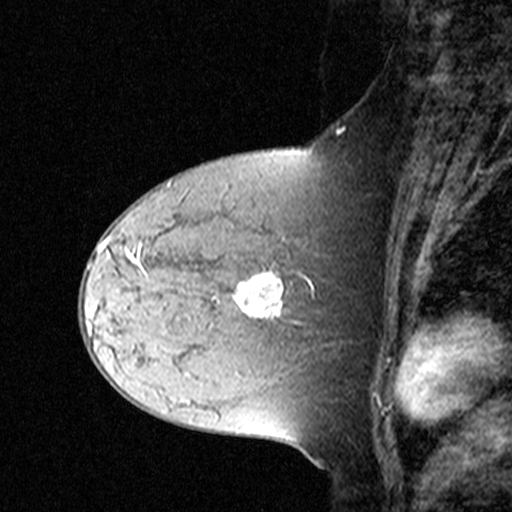
Breast MRI (dynamic contrast-enhanced), one sagittal slice; slice 17 of 44 in the series (ordered by position); dynamic contrast-enhanced study with each time point stored as its own series, time point 2 of 3 at this slice position (early post-contrast, ordered by acquisition time); 1.5 T; TE 4.5 ms, TR 11 ms; 3 mm slice thickness; 512 × 512 image matrix, field of view 200 × 200 mm. Female patient, age 44 years. Case-level facts recorded for this patient, not image findings: setting: breast cancer imaged before/during neoadjuvant chemotherapy; receptor status: triple-negative.
Outlined on this slice (semi-automatically segmented with operator editing):
- analysis volume of interest (the breast-tissue region the enhancement analysis was run in; not a lesion): box from (x=132, y=212) to (x=309, y=331) px
- tumour enhancement mask (voxels above the 90 % enhancement threshold inside the analysis volume of interest): (x=137, y=261)–(x=283, y=316)